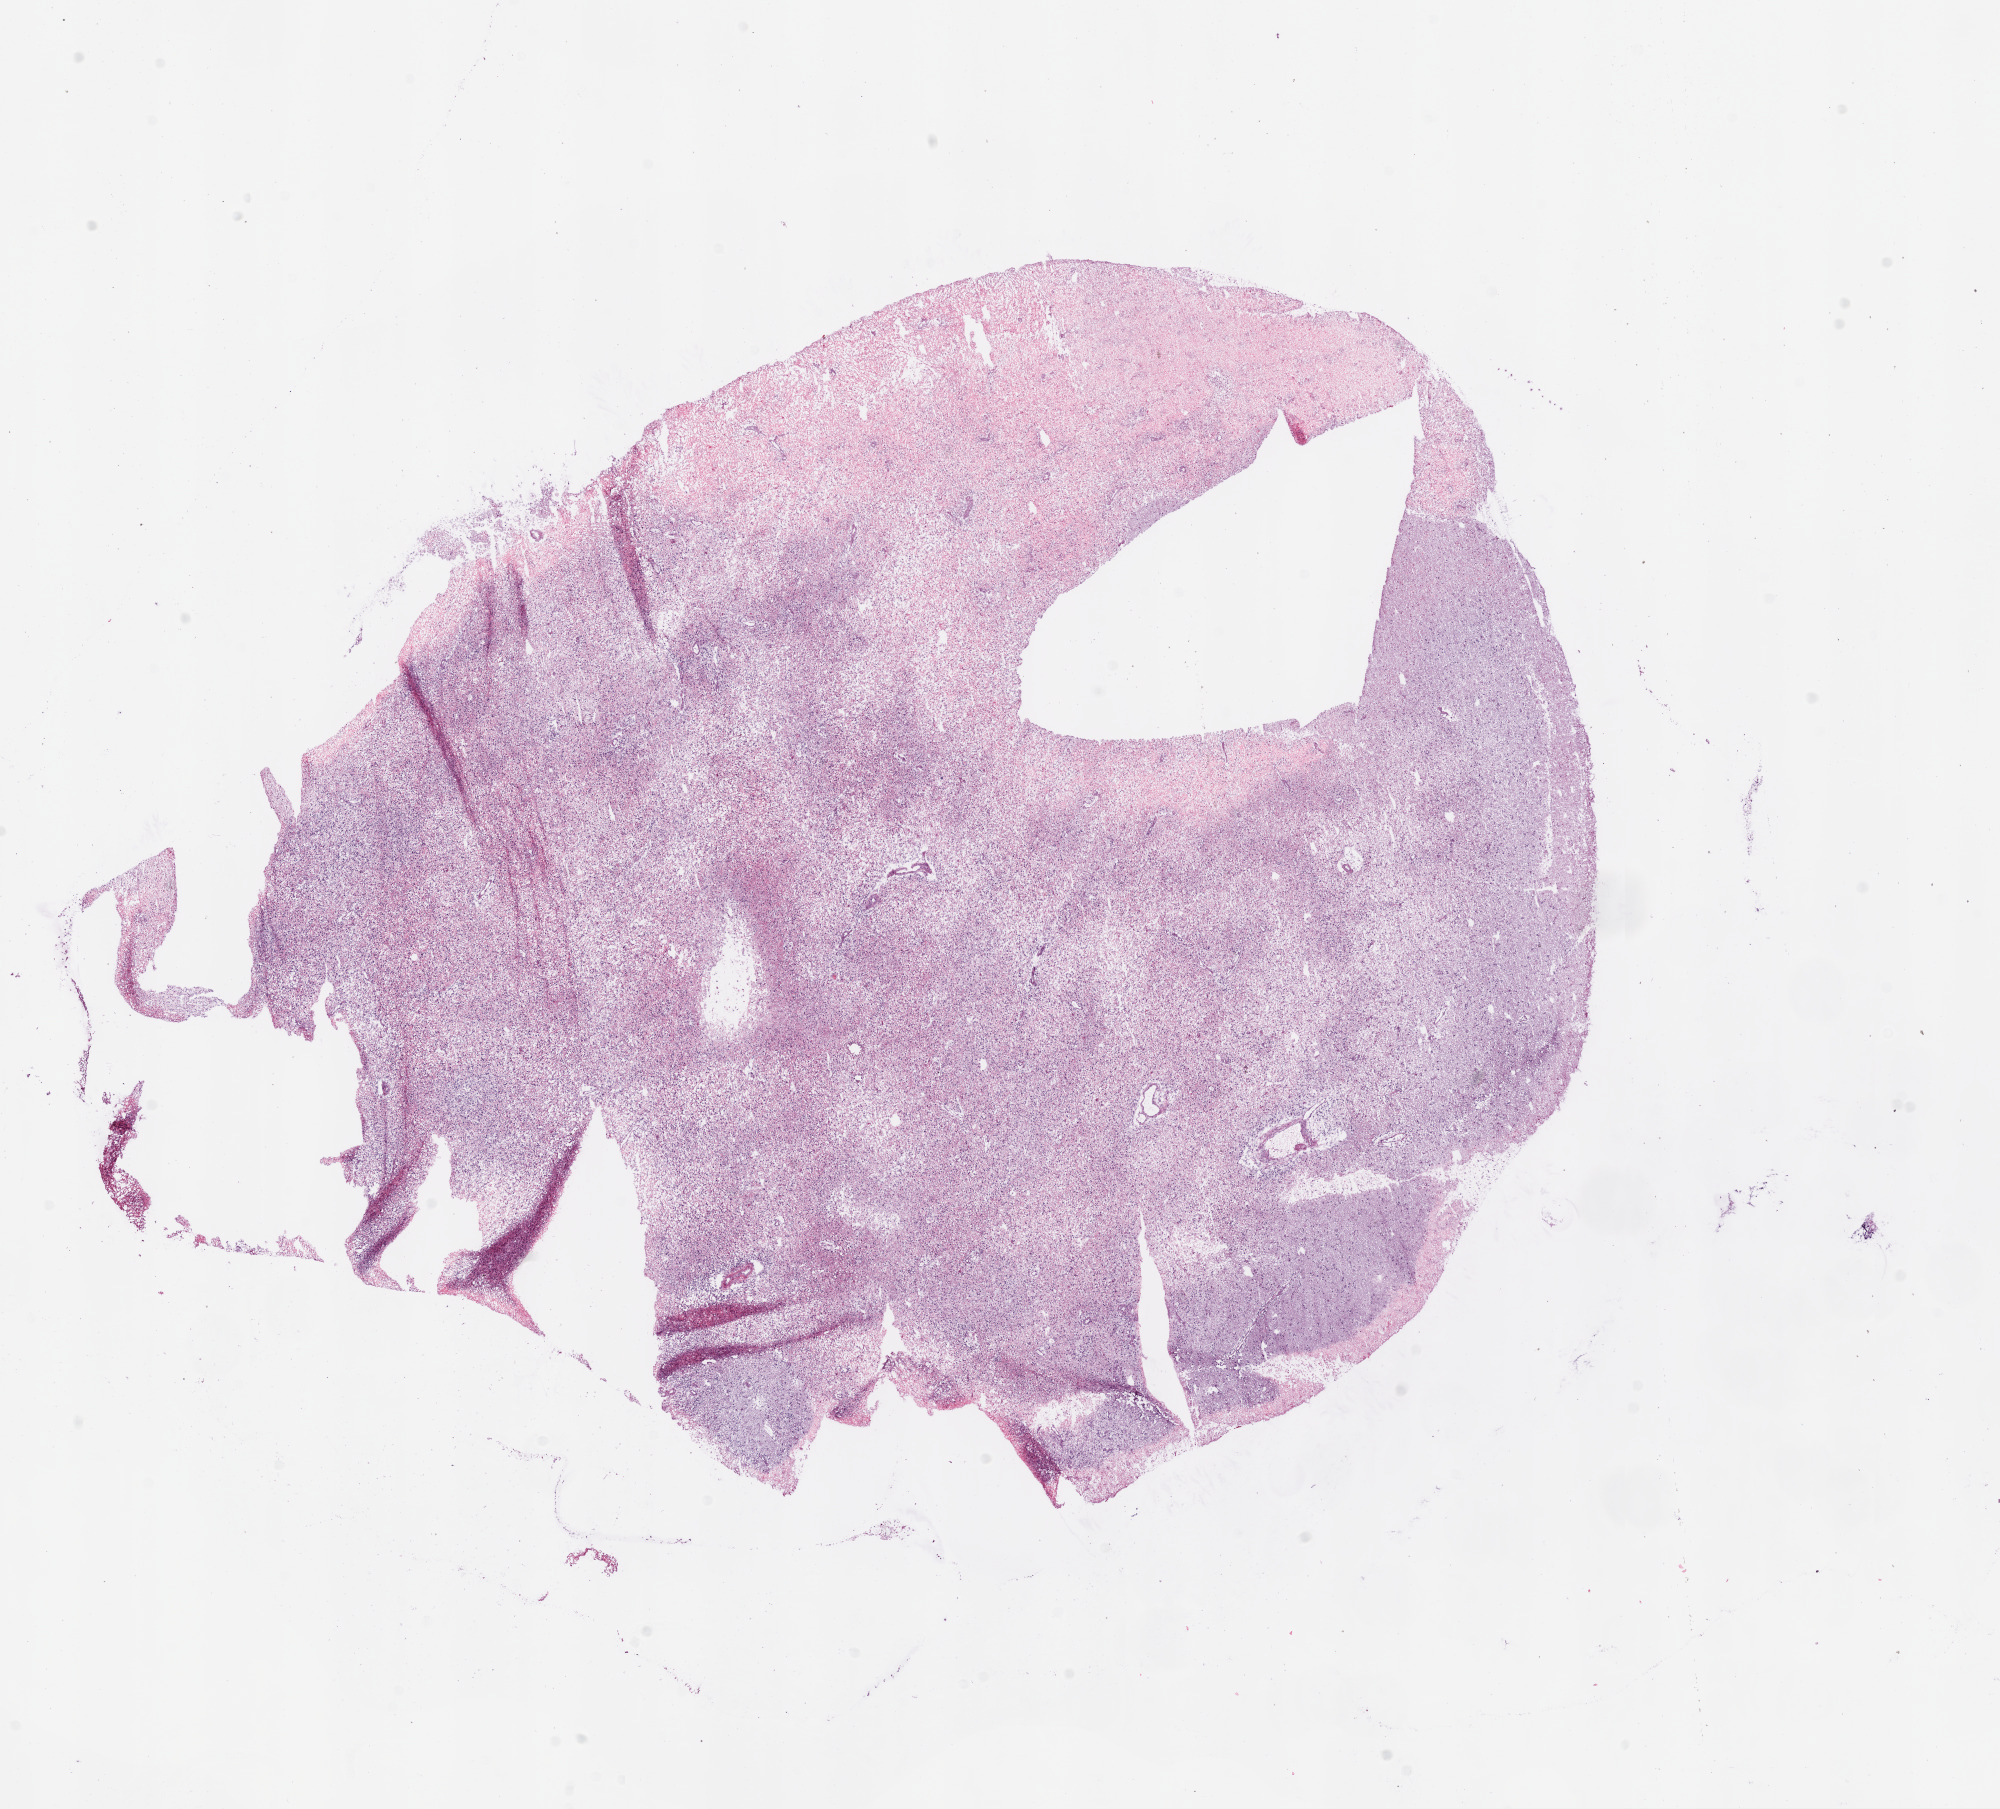
Digitized H&E-stained tissue section (whole slide) — whole scanned area (about 16.0 x 14.5 mm) shown as a low-resolution overview. Frozen section from the bottom of the tissue portion. Sample: primary tumour, brain. Female patient; age at initial diagnosis 62 years. Pathologist review of this section (percent, as recorded): tumour cells 95%, tumour nuclei 80%, normal cells 0%, stromal cells 0%, necrosis 10%.
Pathologic diagnosis: Glioblastoma.